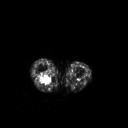
FDG PET of an extremity soft-tissue mass (from a PET/CT study), one axial slice. Slice 185 of 267 in the series (ordered by position). 3.27 mm slice thickness. 128 × 128 image matrix, field of view 500 × 500 mm. Female patient, age 62 years. Case-level facts recorded for this patient, not image findings: histological type: liposarcoma; site of the primary tumour: right thigh.
Structures marked on this image (expert contour drawn on MRI and transferred to this co-registered scan by the dataset authors):
- gross tumour volume (mass): box from (x=38, y=74) to (x=52, y=85) px